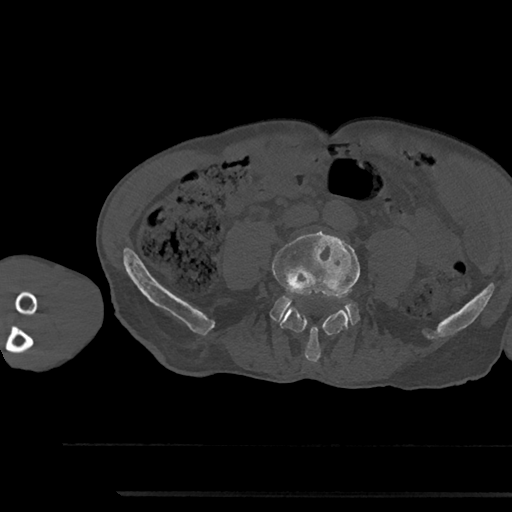
CT including the spine, one axial slice; 120 kVp; bone window (W 1800 / L 400 HU); 0.5 mm slice thickness; 512 × 512 image matrix. Patient: male, 79 years. Case-level facts recorded for this patient, not image findings: primary cancer: prostate.
Outlined on this slice (semi-automatic segmentation, software-assisted and operator-edited):
- L4 vertebra: bounding box (x1, y1, x2, y2) in pixels: (272, 231, 360, 362)
- L5 vertebra: (271, 296, 358, 324)